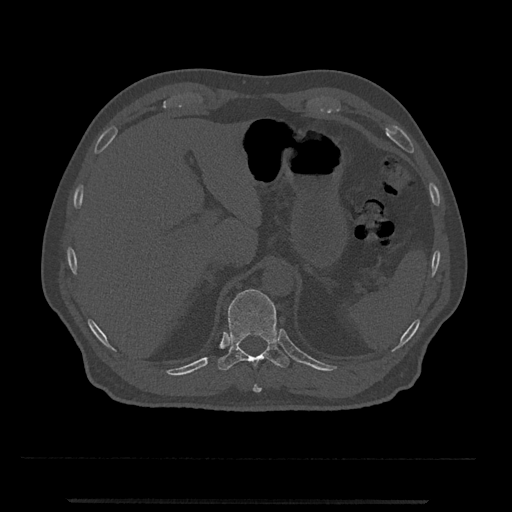
CT including the spine, one axial slice. Position 472 of 797 along the scan axis. Reconstruction kernel Br40s/3. 120 kVp. Bone window (W 1800 / L 400 HU). 0.5 mm slice thickness. 512 × 512 image matrix. Patient: male, 63 years. Case-level facts recorded for this patient, not image findings: primary cancer: prostate.
Annotated regions visible in this slice (semi-automatically segmented with operator editing):
- T10 vertebra: box from (x=253, y=384) to (x=262, y=393) px
- T11 vertebra: (x=217, y=289)–(x=289, y=371)